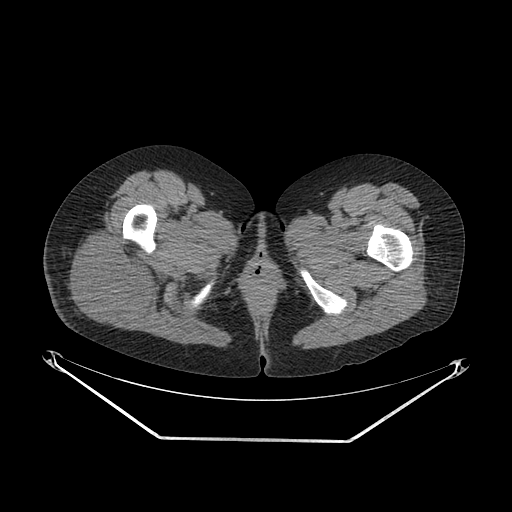
CT of an extremity soft-tissue mass (from a PET/CT study), one axial slice; position 32 of 267 along the scan axis; reconstruction kernel SOFT; 140 kVp; soft-tissue window (W 400 / L 40 HU); 3.75 mm slice thickness; 512 × 512 image matrix, field of view 500 × 500 mm. Female patient. Case-level facts recorded for this patient, not image findings: histological type: epithelioid sarcoma with vascular differentiation; site of the primary tumour: right buttock.
Annotated regions visible in this slice (expert contour drawn on MRI and transferred to this co-registered scan by the dataset authors):
- gross tumour volume (mass): bounding box [x1, y1, x2, y2] px = [66, 233, 152, 323]